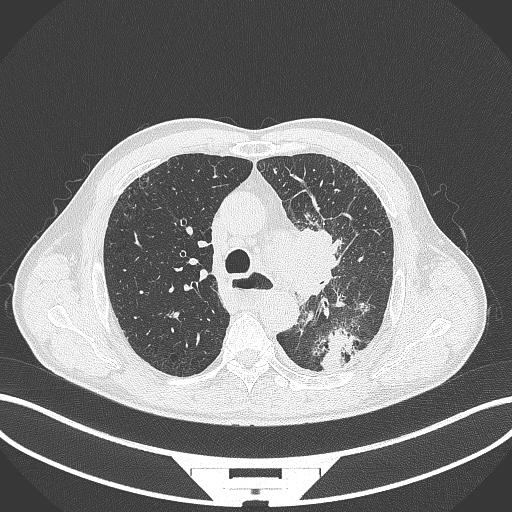
Chest CT, one axial slice. Slice 267 of 411 in the series (ordered by position). 120 kVp. Lung window (W 1500 / L -600 HU). 512 × 512 image matrix, field of view 400 × 400 mm. Patient: male, 57 years. Case-level facts recorded for this patient, not image findings: clinical TNM (as recorded): T2a N1 M0.
Outlined on this slice (bounding box drawn by a radiologist):
- lung tumour (recorded histology: squamous cell carcinoma): bounding box <284,218,344,304> (left, top, right, bottom; pixels)